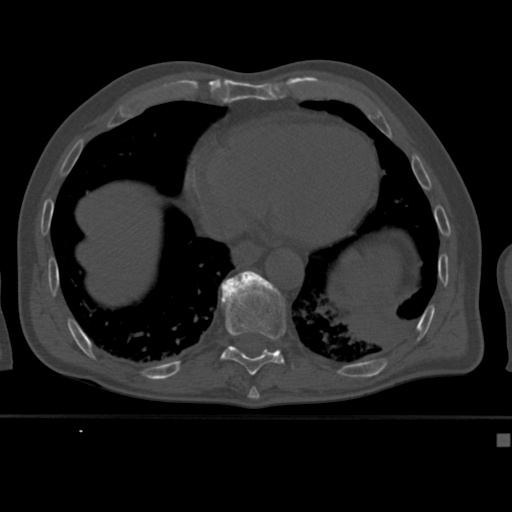
CT including the spine, one axial slice. Slice 227 of 430 in the series (ordered by position). 120 kVp. Bone window (W 1800 / L 400 HU). 1.5 mm slice thickness. 512 × 512 image matrix, field of view 337 × 337 mm. Patient: male, 64 years. Case-level facts recorded for this patient, not image findings: primary cancer: uterus; vertebrae with lytic lesions (as recorded): T1, T4, T5, T7, L5.
Annotated regions visible in this slice (semi-automatic segmentation, software-assisted and operator-edited):
- T10 vertebra: bounding box <220,271,286,375> (left, top, right, bottom; pixels)
- T11 vertebra: <224,271,248,281>